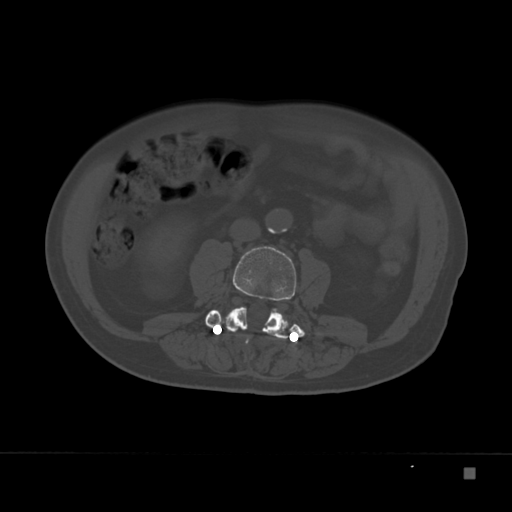
CT including the spine, one axial slice; slice 63 of 332 in the series (ordered by position); 120 kVp; bone window (W 1800 / L 400 HU); 1.5 mm slice thickness; 512 × 512 image matrix, field of view 389 × 389 mm. Male patient, age 72 years. Case-level facts recorded for this patient, not image findings: primary cancer: skeletal.
Annotated regions visible in this slice (semi-automatic segmentation, software-assisted and operator-edited):
- L3 vertebra: bounding box <205,246,305,342> (left, top, right, bottom; pixels)